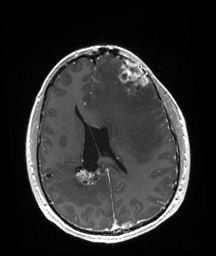
Brain MRI from a brain-tumour surgery series, one axial slice. Position 75 of 192 along the scan axis. T1-weighted post-contrast. 216 × 256 image matrix, field of view 219 × 260 mm. From the clinical record (not read from this slice): tumour location: Left Frontal.
Outlined on this slice (manually delineated by an expert):
- tumour: box from (x=118, y=60) to (x=149, y=96) px